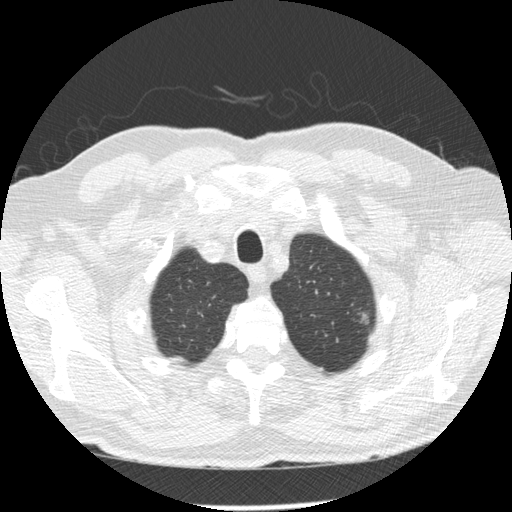
Low-dose screening chest CT, axial slice, third annual screen, lung window (W 1500 / L -600 HU), 120 kVp, slice 26 of 258 in the series, 512 × 512 image matrix, field of view 360 × 360 mm. Male participant, aged 73 years at enrolment. Former smoker at enrolment.
Expert-annotated lung lesion, bounding box <352,300,389,341> (left, top, right, bottom; pixels). Screening reader's record for this exam (one nodule recorded; not confirmed to be the boxed lesion): non-calcified nodule or mass ≥4 mm, left upper lobe, 8 × 7 mm, poorly defined margins, mixed attenuation, pre-existing on the prior screen: no. Official screen result: positive, other. Lung cancer was diagnosed 93 days after this screen: adenocarcinoma, NOS, left upper lobe, poorly differentiated (G3), stage IB (AJCC 6th edition), 10 mm at pathology.